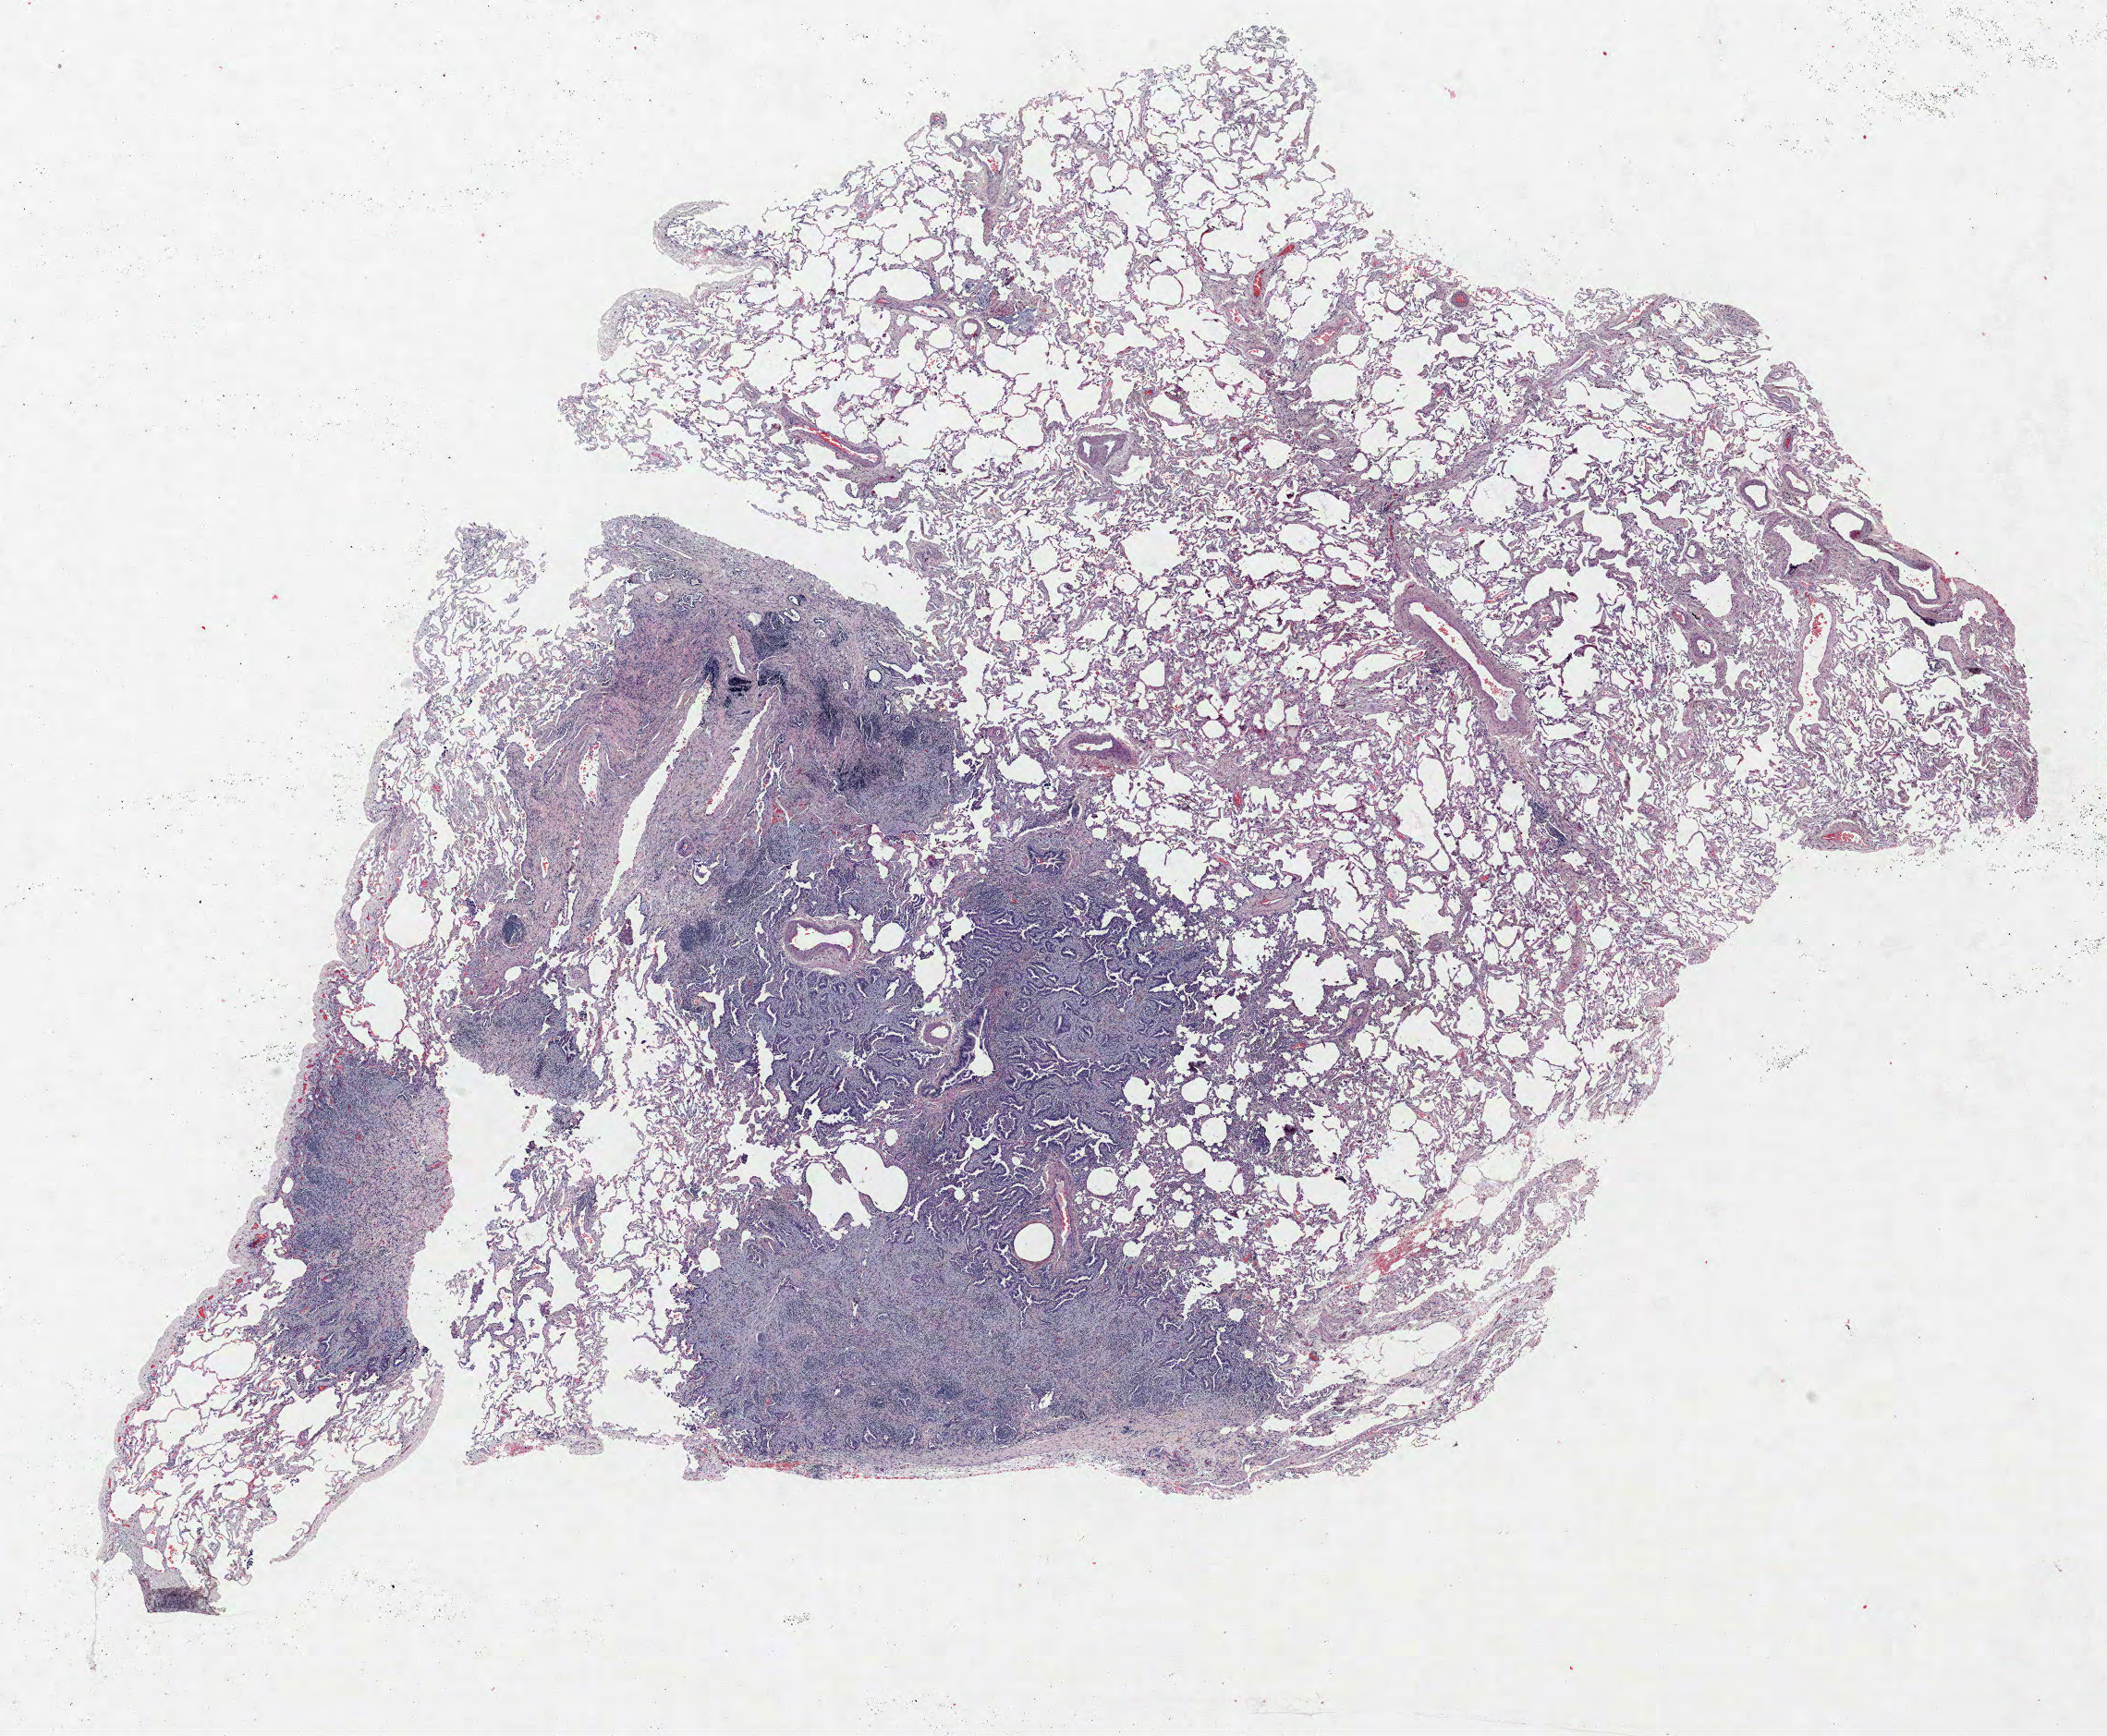
Whole-slide histology image, Hematoxylin and eosin (H&E) stained, low-resolution overview of the scanned area, about 18.2 x 15.0 mm (from a 40x scan); FFPE section; lung. Female, age 56 at enrolment. Grade: moderately differentiated (G2).
ICD-O-3 topography: upper lobe of lung (C34.1). Tumour size (pathology): 10 mm. Participant's lung-cancer diagnosis: Adenocarcinoma, NOS. Primary tumour location (clinical record): left upper lobe. Stage (AJCC 6th edition): IA.